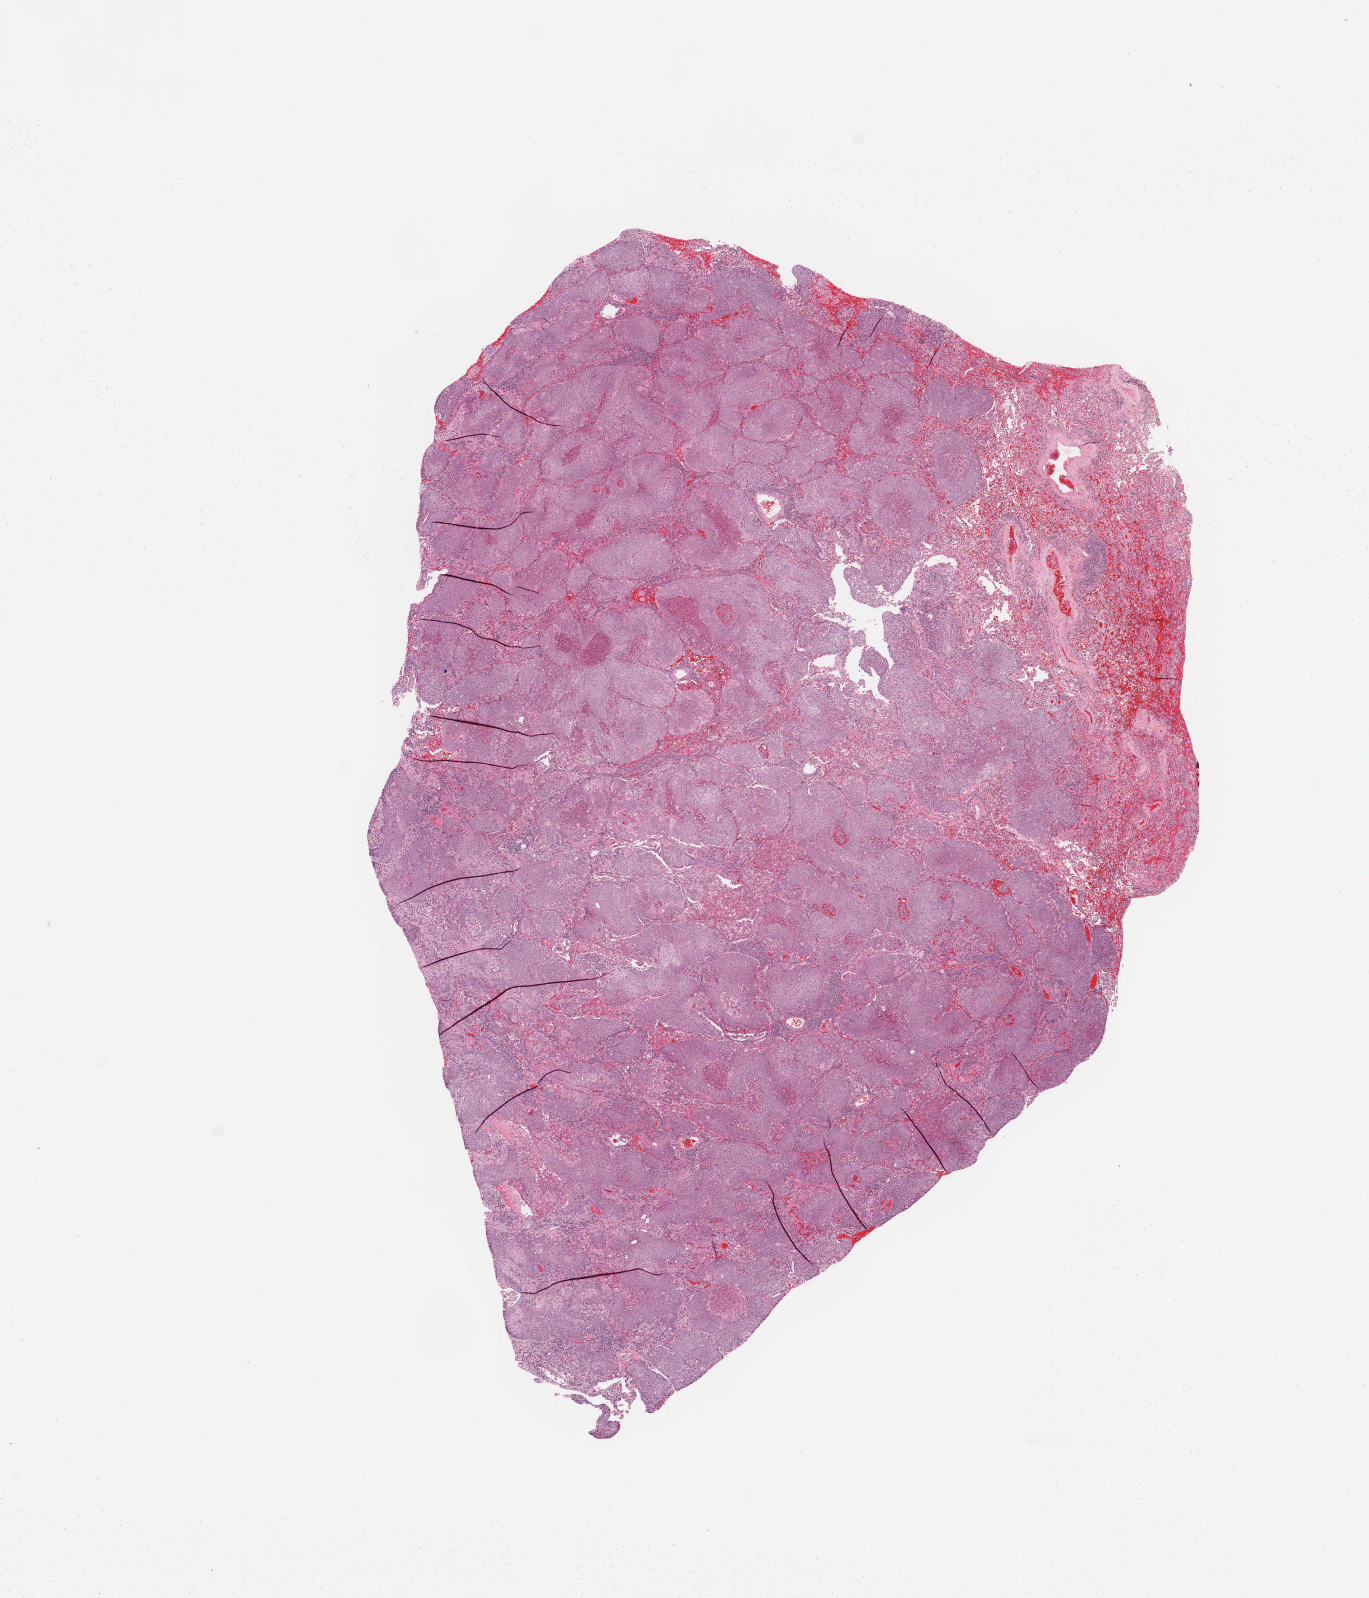
H&E whole-slide image, whole scanned area (about 10.8 x 12.6 mm) shown as a low-resolution overview. Tumour tissue sample, sampled site: lung. Male, 58 y/o. Histologic grade: G3 (poorly differentiated). Slide review estimates, as recorded: tumour nuclei 85%, necrosis 10%.
* primary tumour site (as recorded): right lower lobe
* histologic diagnosis: Squamous cell carcinoma, NOS
* AJCC pathologic stage: IIA